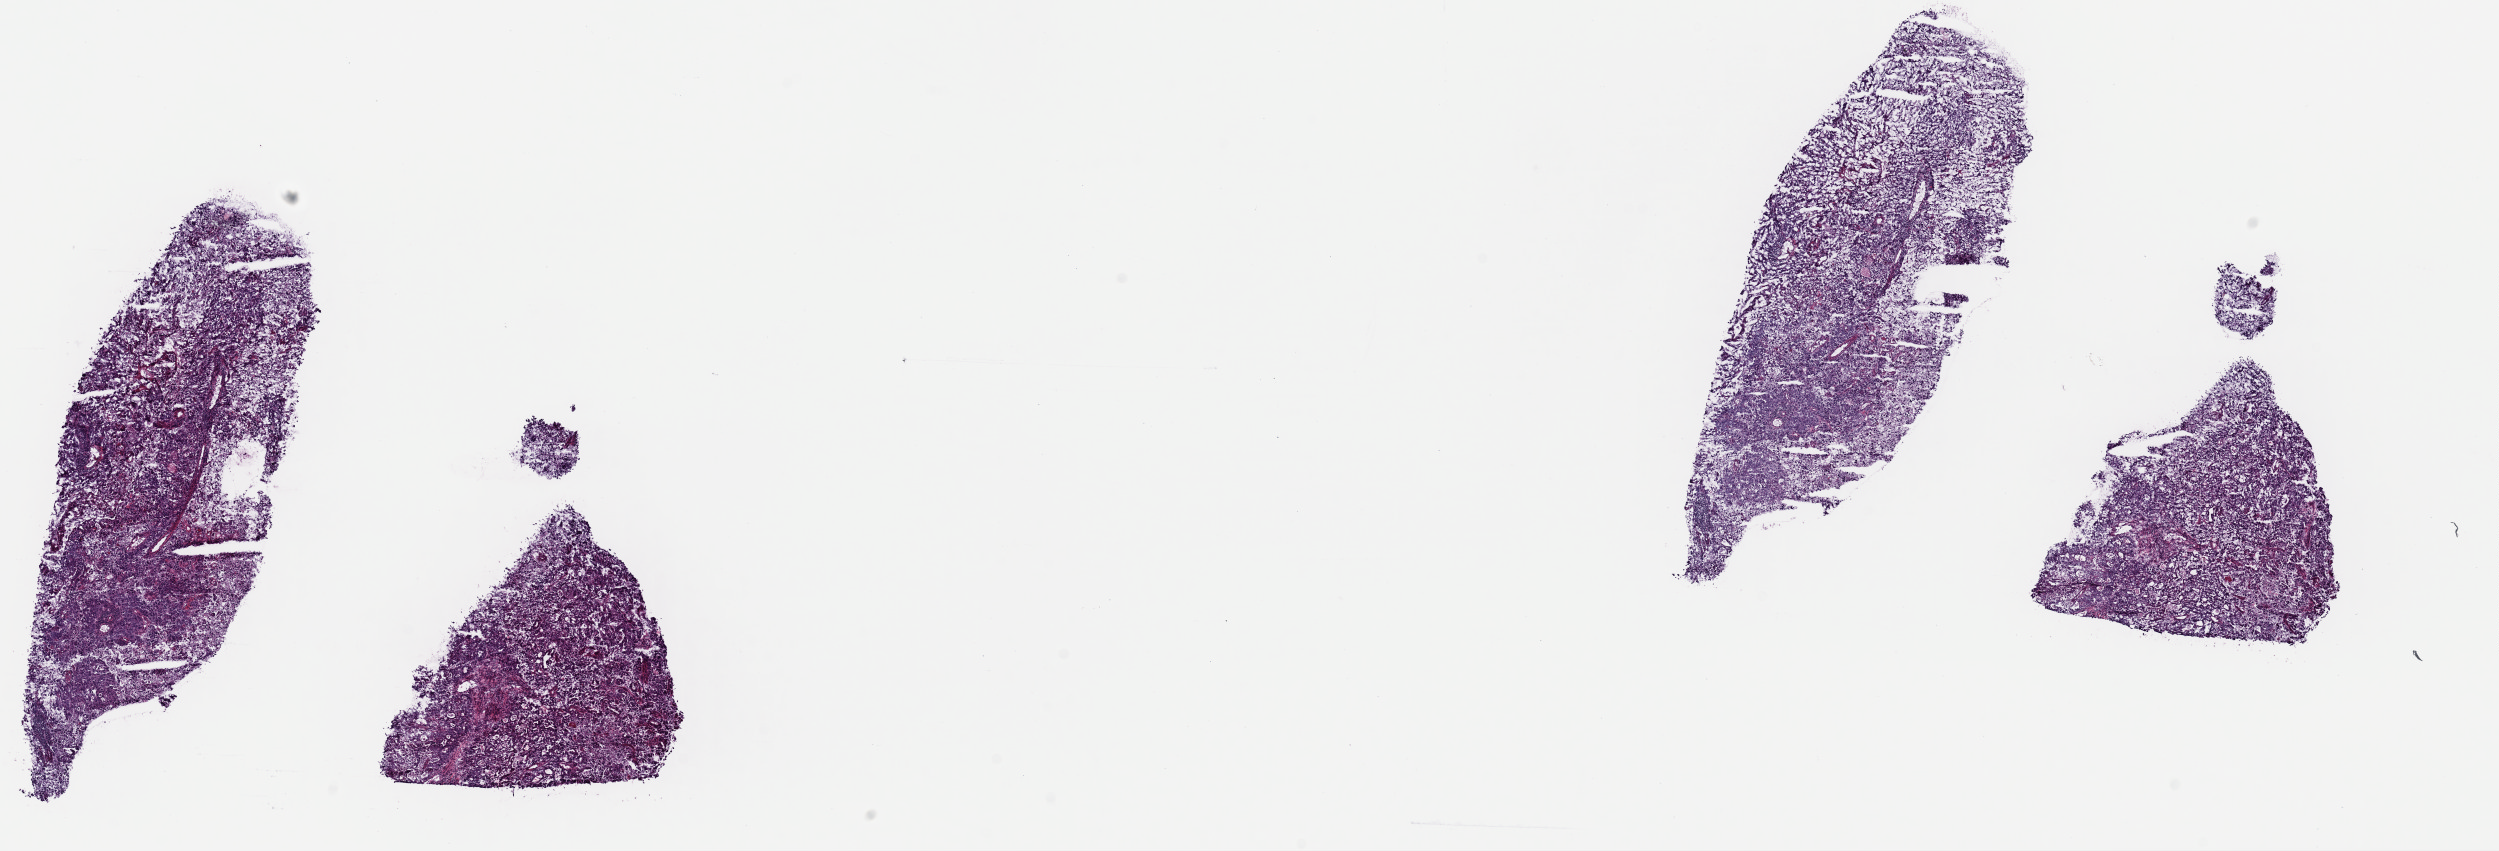
Whole-slide histology image, Hematoxylin and eosin (H&E) stained, a low-resolution overview of the entire scanned area, about 19.7 x 6.7 mm (from a 40x scan), frozen section, uterus, primary tumour sample. Female patient; age at initial diagnosis 66 years. Histologic grade: G3 (poorly differentiated). Pathologist review of this section (percent, as recorded): tumour cells 70%, tumour nuclei 70%, normal cells 0%, stromal cells 20%, necrosis 10%. Infiltration values recorded for this section: lymphocyte infiltration 40%, monocyte infiltration 20%, neutrophil infiltration 20%.
* pathologic diagnosis: Endometrioid adenocarcinoma, NOS
* FIGO stage: IIIC1